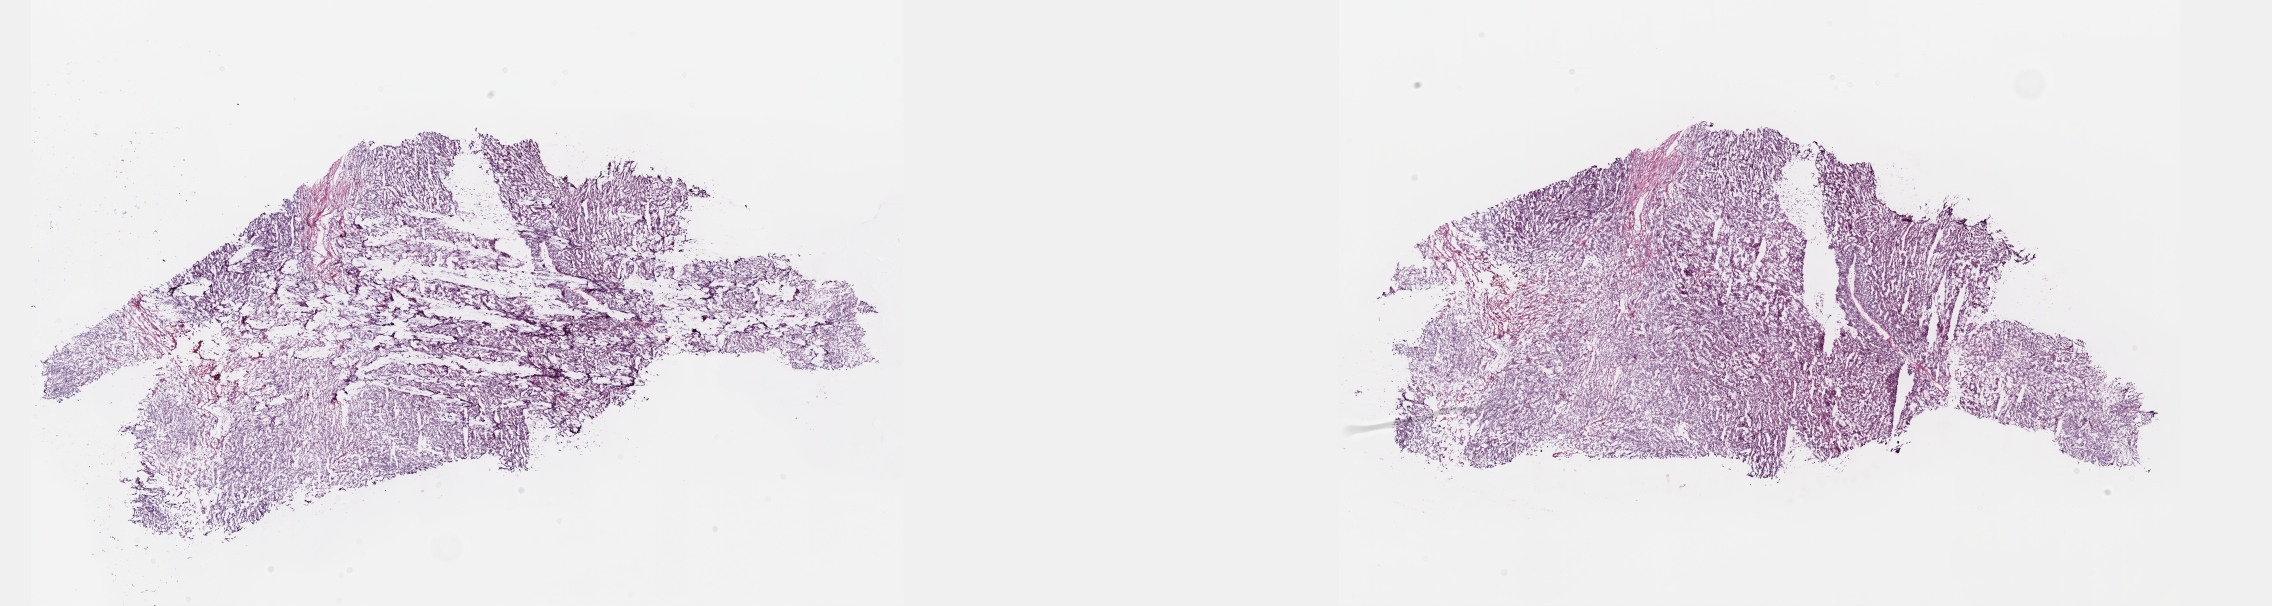
Hematoxylin and eosin (H&E) stained whole-slide image, a low-resolution overview of the entire scanned area, about 36.7 x 9.8 mm (acquisition: 40x scan), frozen section, sample: primary tumour, kidney. Female, age 75 years at initial diagnosis.
Pathologic diagnosis: Papillary adenocarcinoma, NOS.